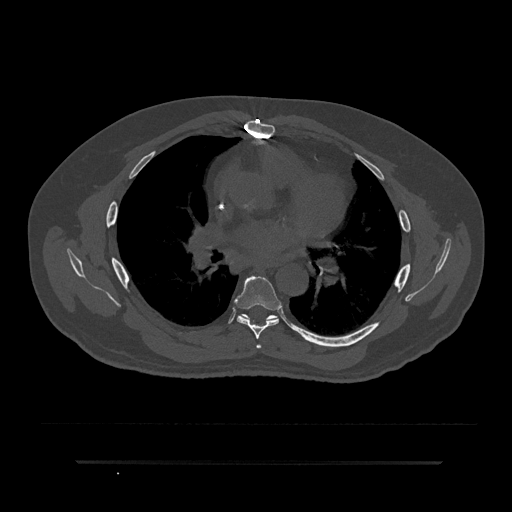
CT including the spine, one axial slice; reconstruction kernel Br40s/3; 120 kVp; bone window (W 1800 / L 400 HU); 0.5 mm slice thickness; 512 × 512 image matrix, field of view 464 × 464 mm. Male patient, age 59 years. Case-level facts recorded for this patient, not image findings: primary cancer: bile ducts.
Outlined on this slice (semi-automatically segmented with operator editing):
- T5 vertebra: bounding box <256,344,262,349> (left, top, right, bottom; pixels)
- T6 vertebra: <234,276,281,339>
- T7 vertebra: <270,315,274,318>